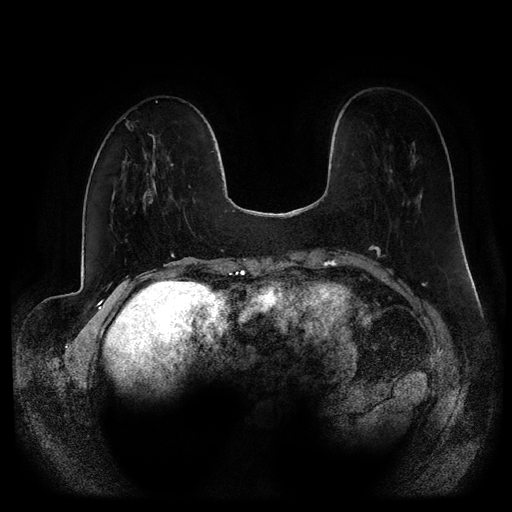
Breast MRI (dynamic contrast-enhanced, multi-phase), one axial slice. Position 29 of 116 along the scan axis. Dynamic contrast-enhanced series, time point 2 of 5 at this slice position (early post-contrast). 1.5 T. TE 2.6 ms, TR 5.2 ms. 512 × 512 image matrix, field of view 380 × 380 mm. Female patient, age 53 years.
Annotated regions visible in this slice (semi-automatically segmented with operator editing):
- breast lesion (labelled 'tumour' in the annotation; benign lesions carry a separate 'benign' label): bounding box (x1, y1, x2, y2) in pixels: (125, 120, 139, 131)